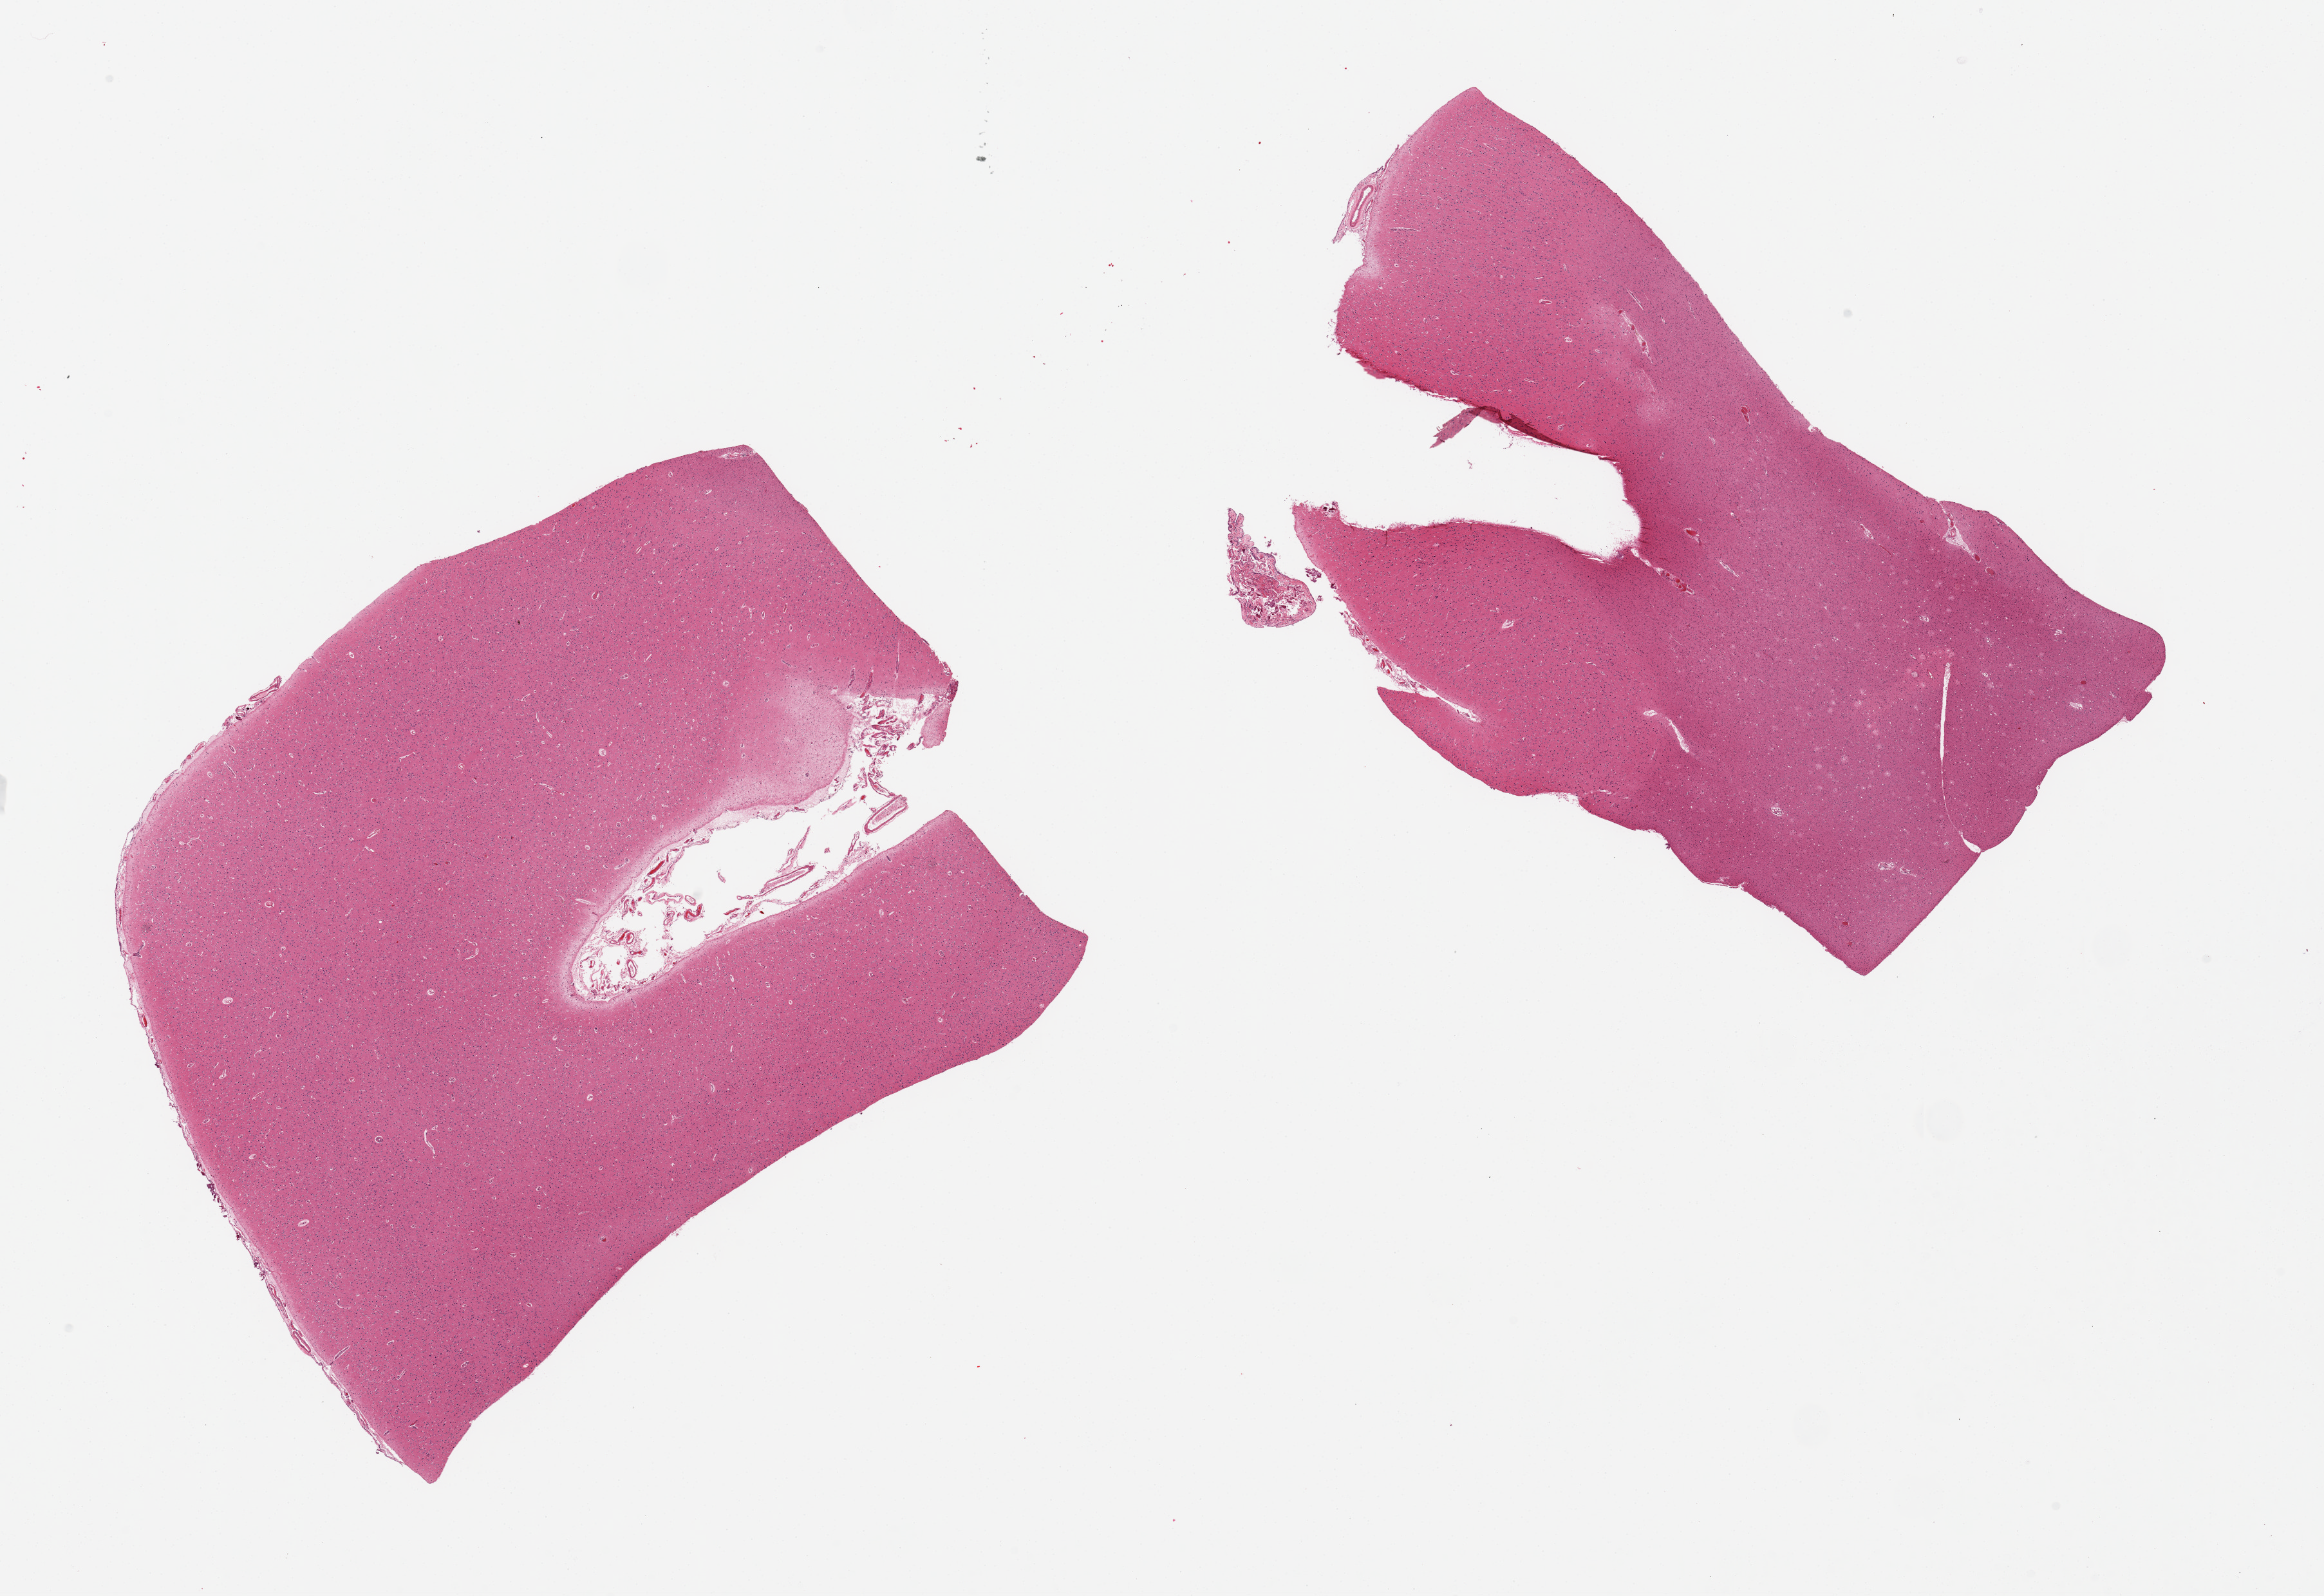
Whole-slide image, hematoxylin and eosin (H&E) stain, brightfield, low-resolution overview of the scanned area, about 28.5 x 19.6 mm (acquisition: 20x scan). PAXgene-fixed paraffin-embedded (PFPE) section. Target tissue: cerebral cortex. Donor tissue sample.
Pathologist's review note for this sample: 2 pieces; small amount of meninges present.